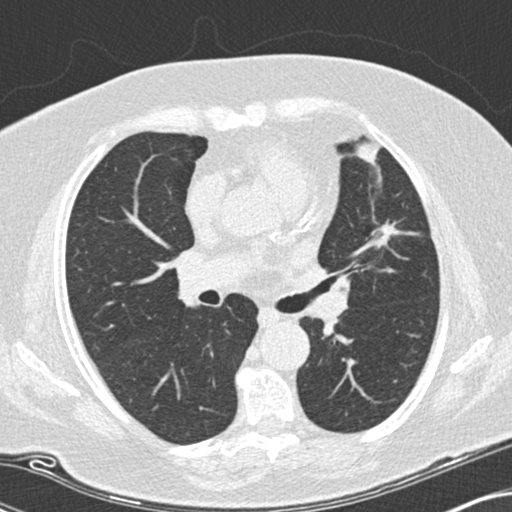
Low-dose screening chest CT, one axial slice. Slice 93 of 151 in the series (ordered by position). Reconstruction kernel B30f. 120 kVp. Lung window (W 1500 / L -600 HU). 512 × 512 image matrix, field of view 330 × 330 mm.
Structures marked on this image (manually delineated by an expert):
- lesion 1 (tumor, upper lobe of left lung): bounding box [x1, y1, x2, y2] px = [367, 223, 396, 247]